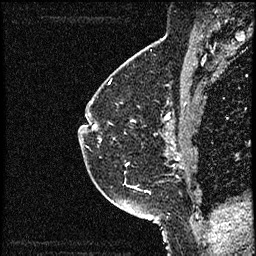
Breast MRI (dynamic contrast-enhanced), one sagittal slice. Position 39 of 52 along the scan axis. Dynamic contrast-enhanced study with each time point stored as its own series, time point 2 of 3 at this slice position (early post-contrast, ordered by acquisition time). 1.5 T. TE 4.2 ms, TR 17.6 ms. 2 mm slice thickness. 256 × 256 image matrix, field of view 200 × 200 mm. Female patient, age 49 years. Case-level facts recorded for this patient, not image findings: setting: breast cancer imaged before/during neoadjuvant chemotherapy; receptor status: HER2-positive.
Structures marked on this image (semi-automatically segmented with operator editing):
- analysis volume of interest (the breast-tissue region the enhancement analysis was run in; not a lesion): bounding box [x1, y1, x2, y2] px = [85, 65, 182, 175]
- tumour enhancement mask (voxels above the 100 % enhancement threshold inside the analysis volume of interest): [93, 125, 181, 160]